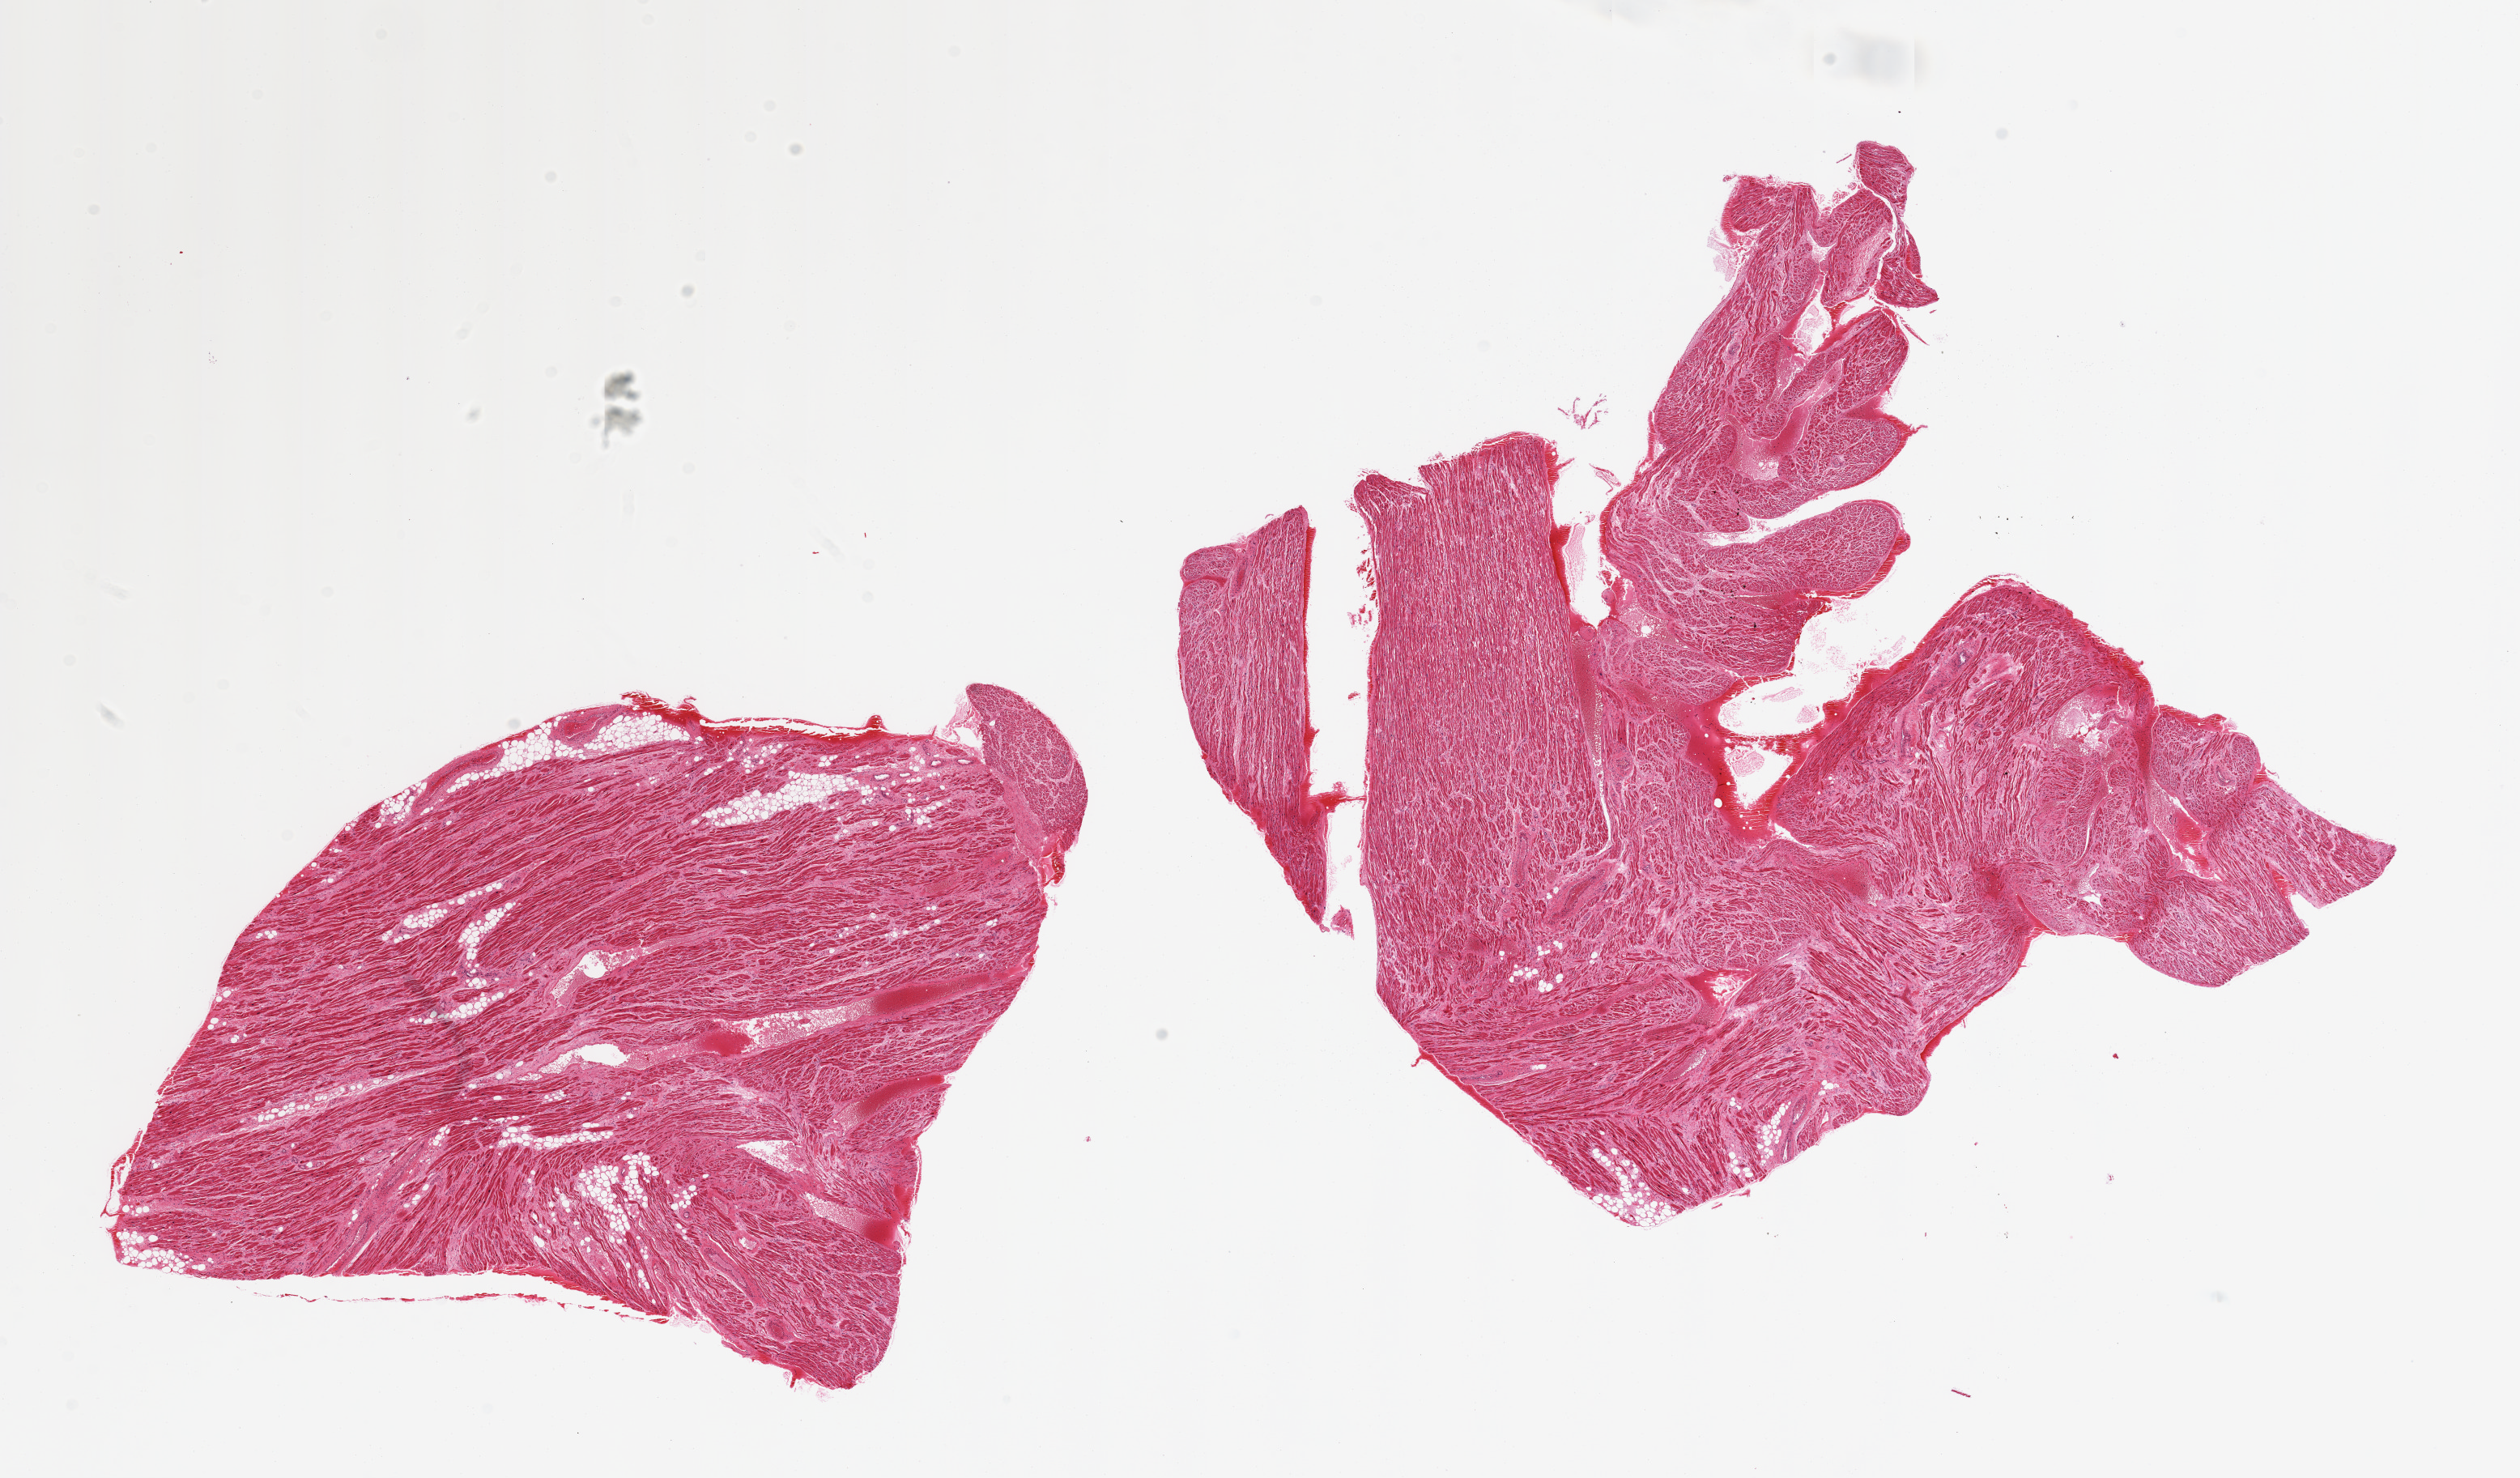
Whole-slide image, haematoxylin and eosin stain — whole scanned area (about 24.6 x 14.4 mm, acquisition: 20x scan) shown as a low-resolution overview. PAXgene-fixed, paraffin-embedded tissue. Sampled site (target tissue): auricular appendage. Donor tissue sample. Donor: male.
Pathologist's review note for this sample: 2 pieces, atrial appendage with interstitial fibrosis and hypertrophy of myocytes.